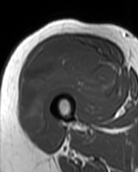
MRI of an extremity soft-tissue mass, one axial slice. Slice 41 of 99 in the series (ordered by position). MR volume resampled by the dataset authors to the PET/CT grid (not the native acquisition matrix). 138 × 172 image matrix. Female patient. From the clinical record (not read from this slice): histological type: pleiomorphic undifferentiated sarcoma; grade: high; site of the primary tumour: right quadricep.
Annotated regions visible in this slice (expert contour drawn on MRI and transferred to this co-registered scan by the dataset authors):
- gross tumour volume including surrounding oedema: box from (x=21, y=39) to (x=118, y=131) px
- gross tumour volume (mass): (x=21, y=39)–(x=118, y=131)